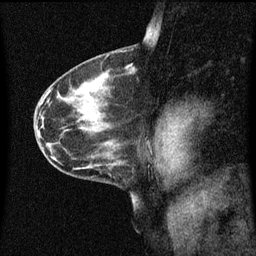
Breast MRI (dynamic contrast-enhanced), one sagittal slice. Slice 36 of 60 in the series (ordered by position). Dynamic contrast-enhanced series, image 2 of 3 at this slice position (ordered by acquisition). 1.5 T. TE 4.2 ms, TR 8.4 ms. 256 × 256 image matrix. Patient: female, 41 years.
Annotated regions visible in this slice (semi-automatic segmentation, software-assisted and operator-edited):
- analysis volume of interest (the breast-tissue region the enhancement analysis was run in; not a lesion): bounding box <121,58,141,81> (left, top, right, bottom; pixels)
- tumour enhancement mask (voxels above the 70 % enhancement threshold inside the analysis volume of interest): <127,64,134,75>